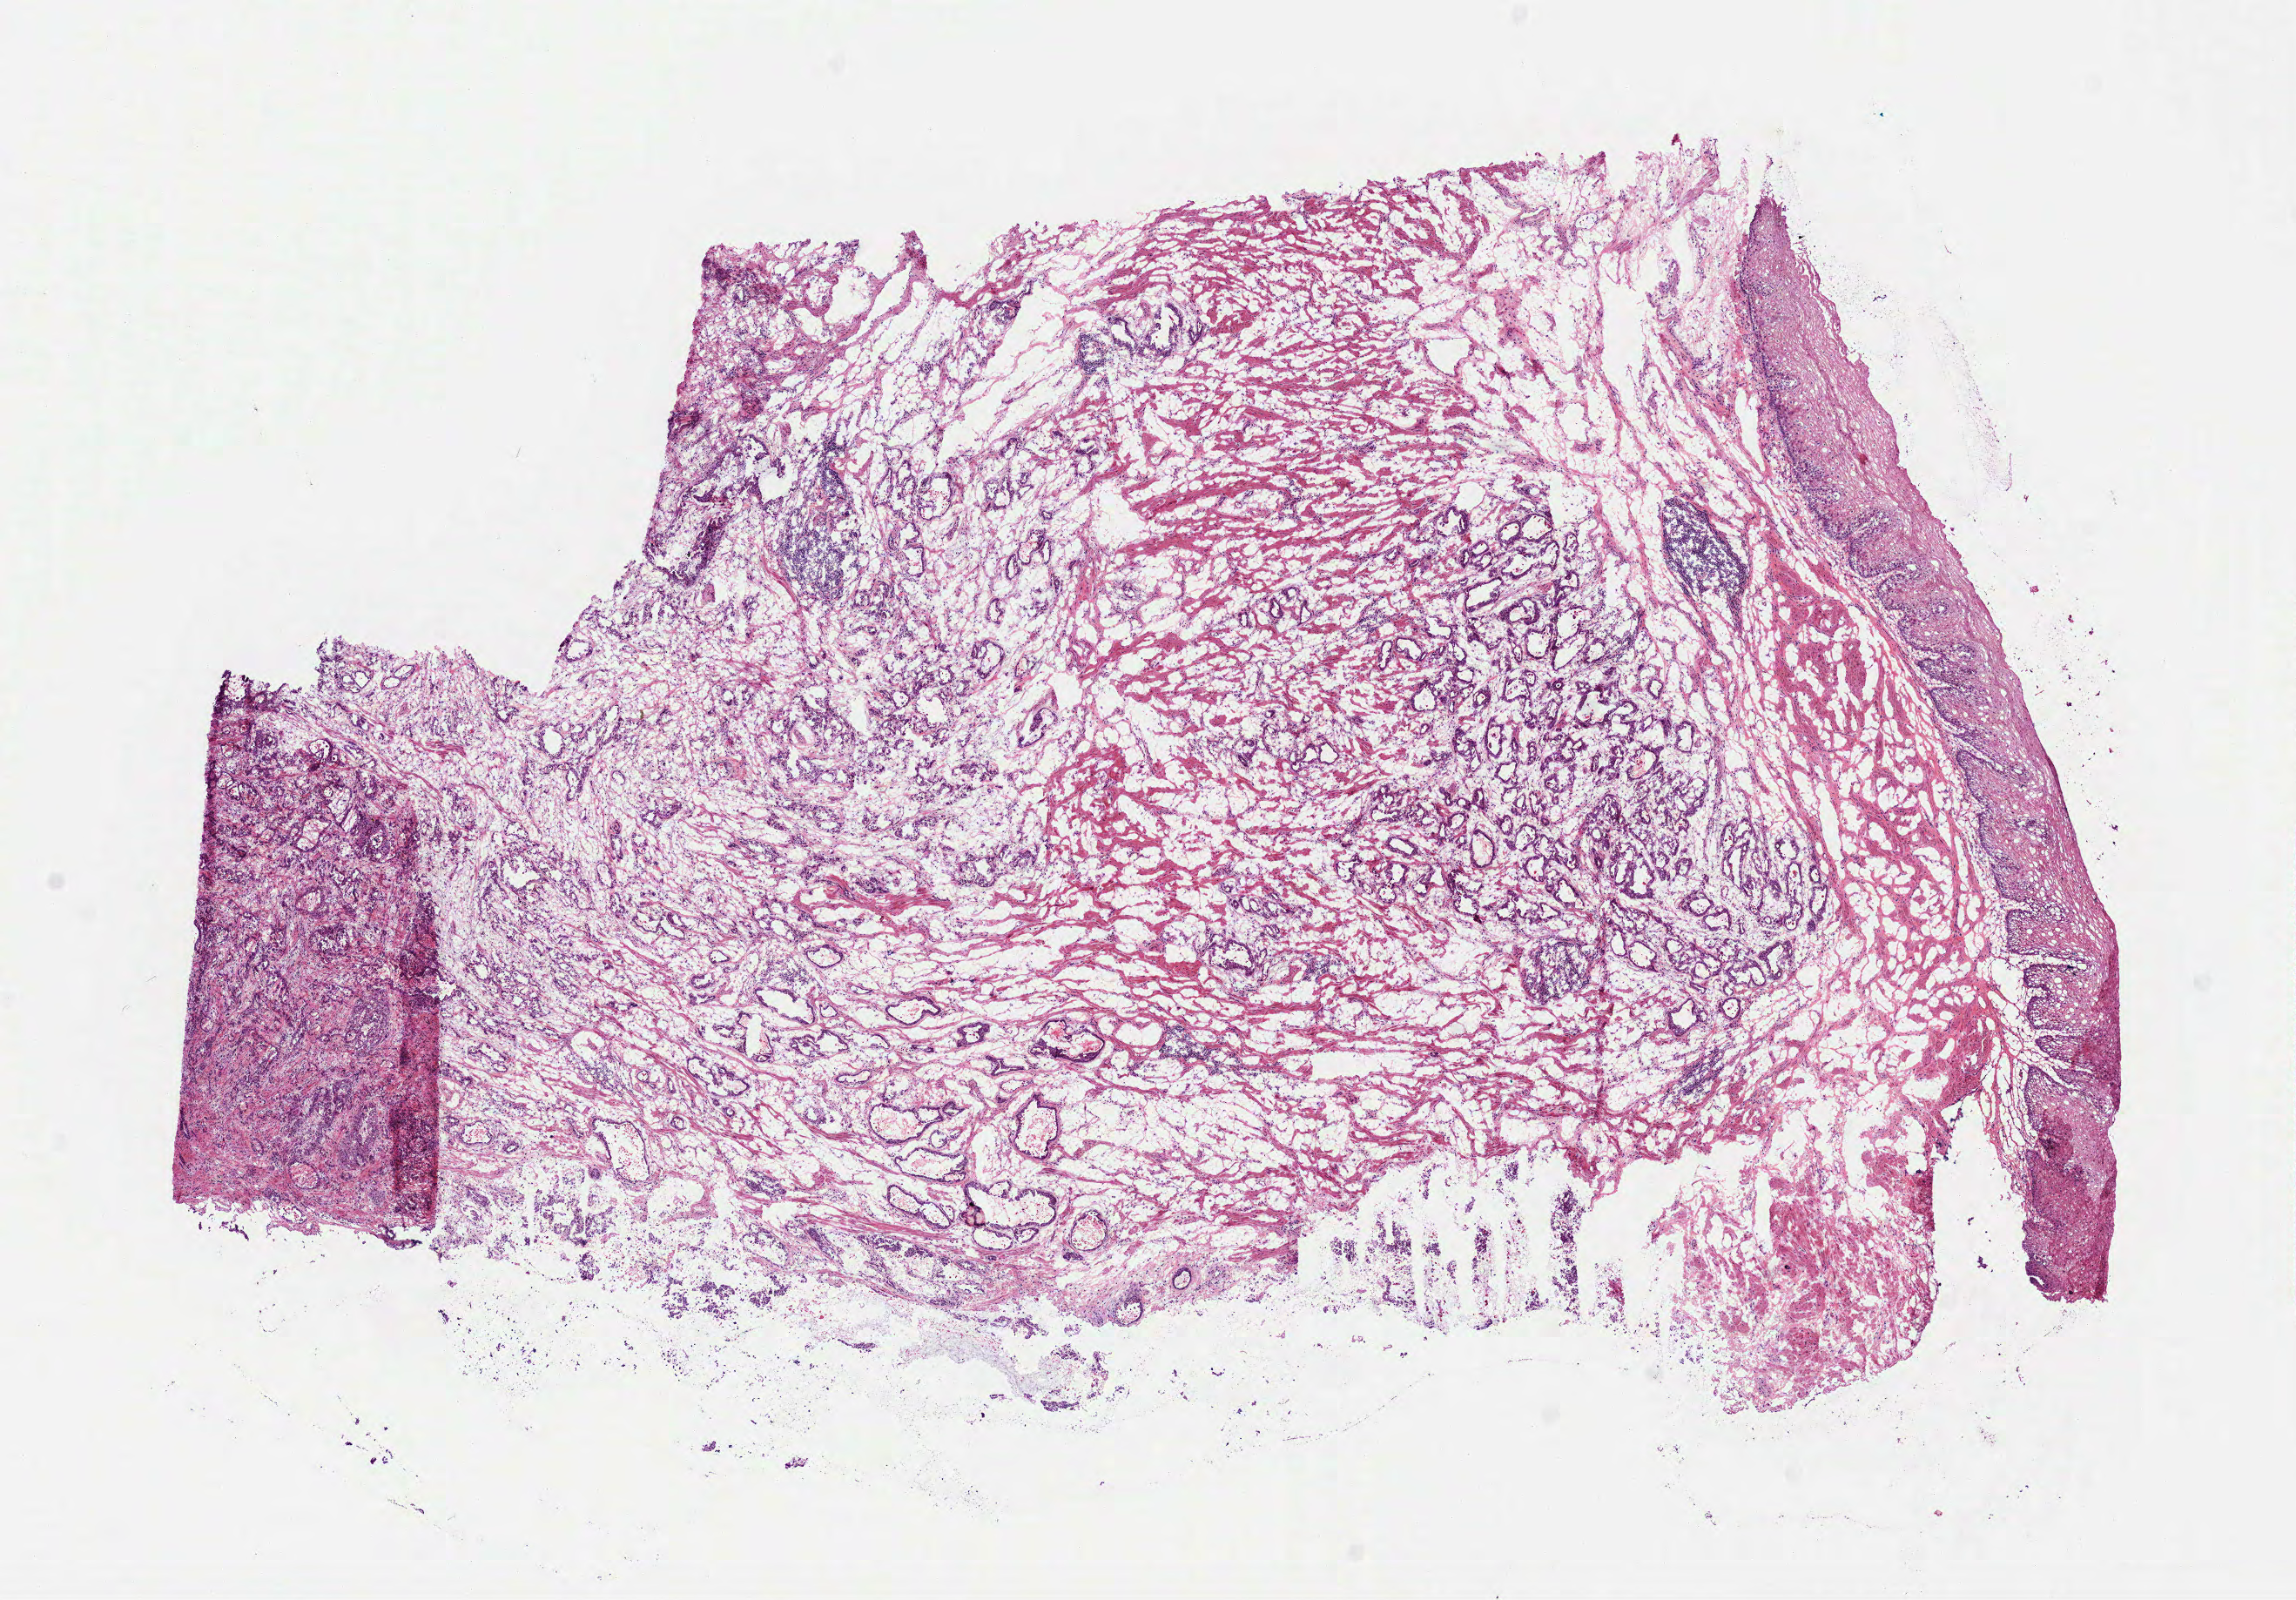
Whole-slide histology image, H&E-stained — a low-resolution overview of the entire scanned area, about 10.6 x 7.4 mm (acquisition: 40x scan), frozen section from the top of the tissue portion, sample: primary tumour, stomach. Male, age 50 years at initial diagnosis. Histologic grade: G3 (poorly differentiated). Composition of this section per pathologist review: tumour cells 74%, tumour nuclei 65%, normal cells 13%, stromal cells 13%, necrosis 0%. Infiltration values recorded for this section: lymphocyte infiltration 20%, monocyte infiltration 0%, neutrophil infiltration 5%.
- lymph nodes positive (case pathology): 2 of 17 examined
- histologic diagnosis: Carcinoma, diffuse type (cardia, NOS)
- AJCC pathologic stage: IIB